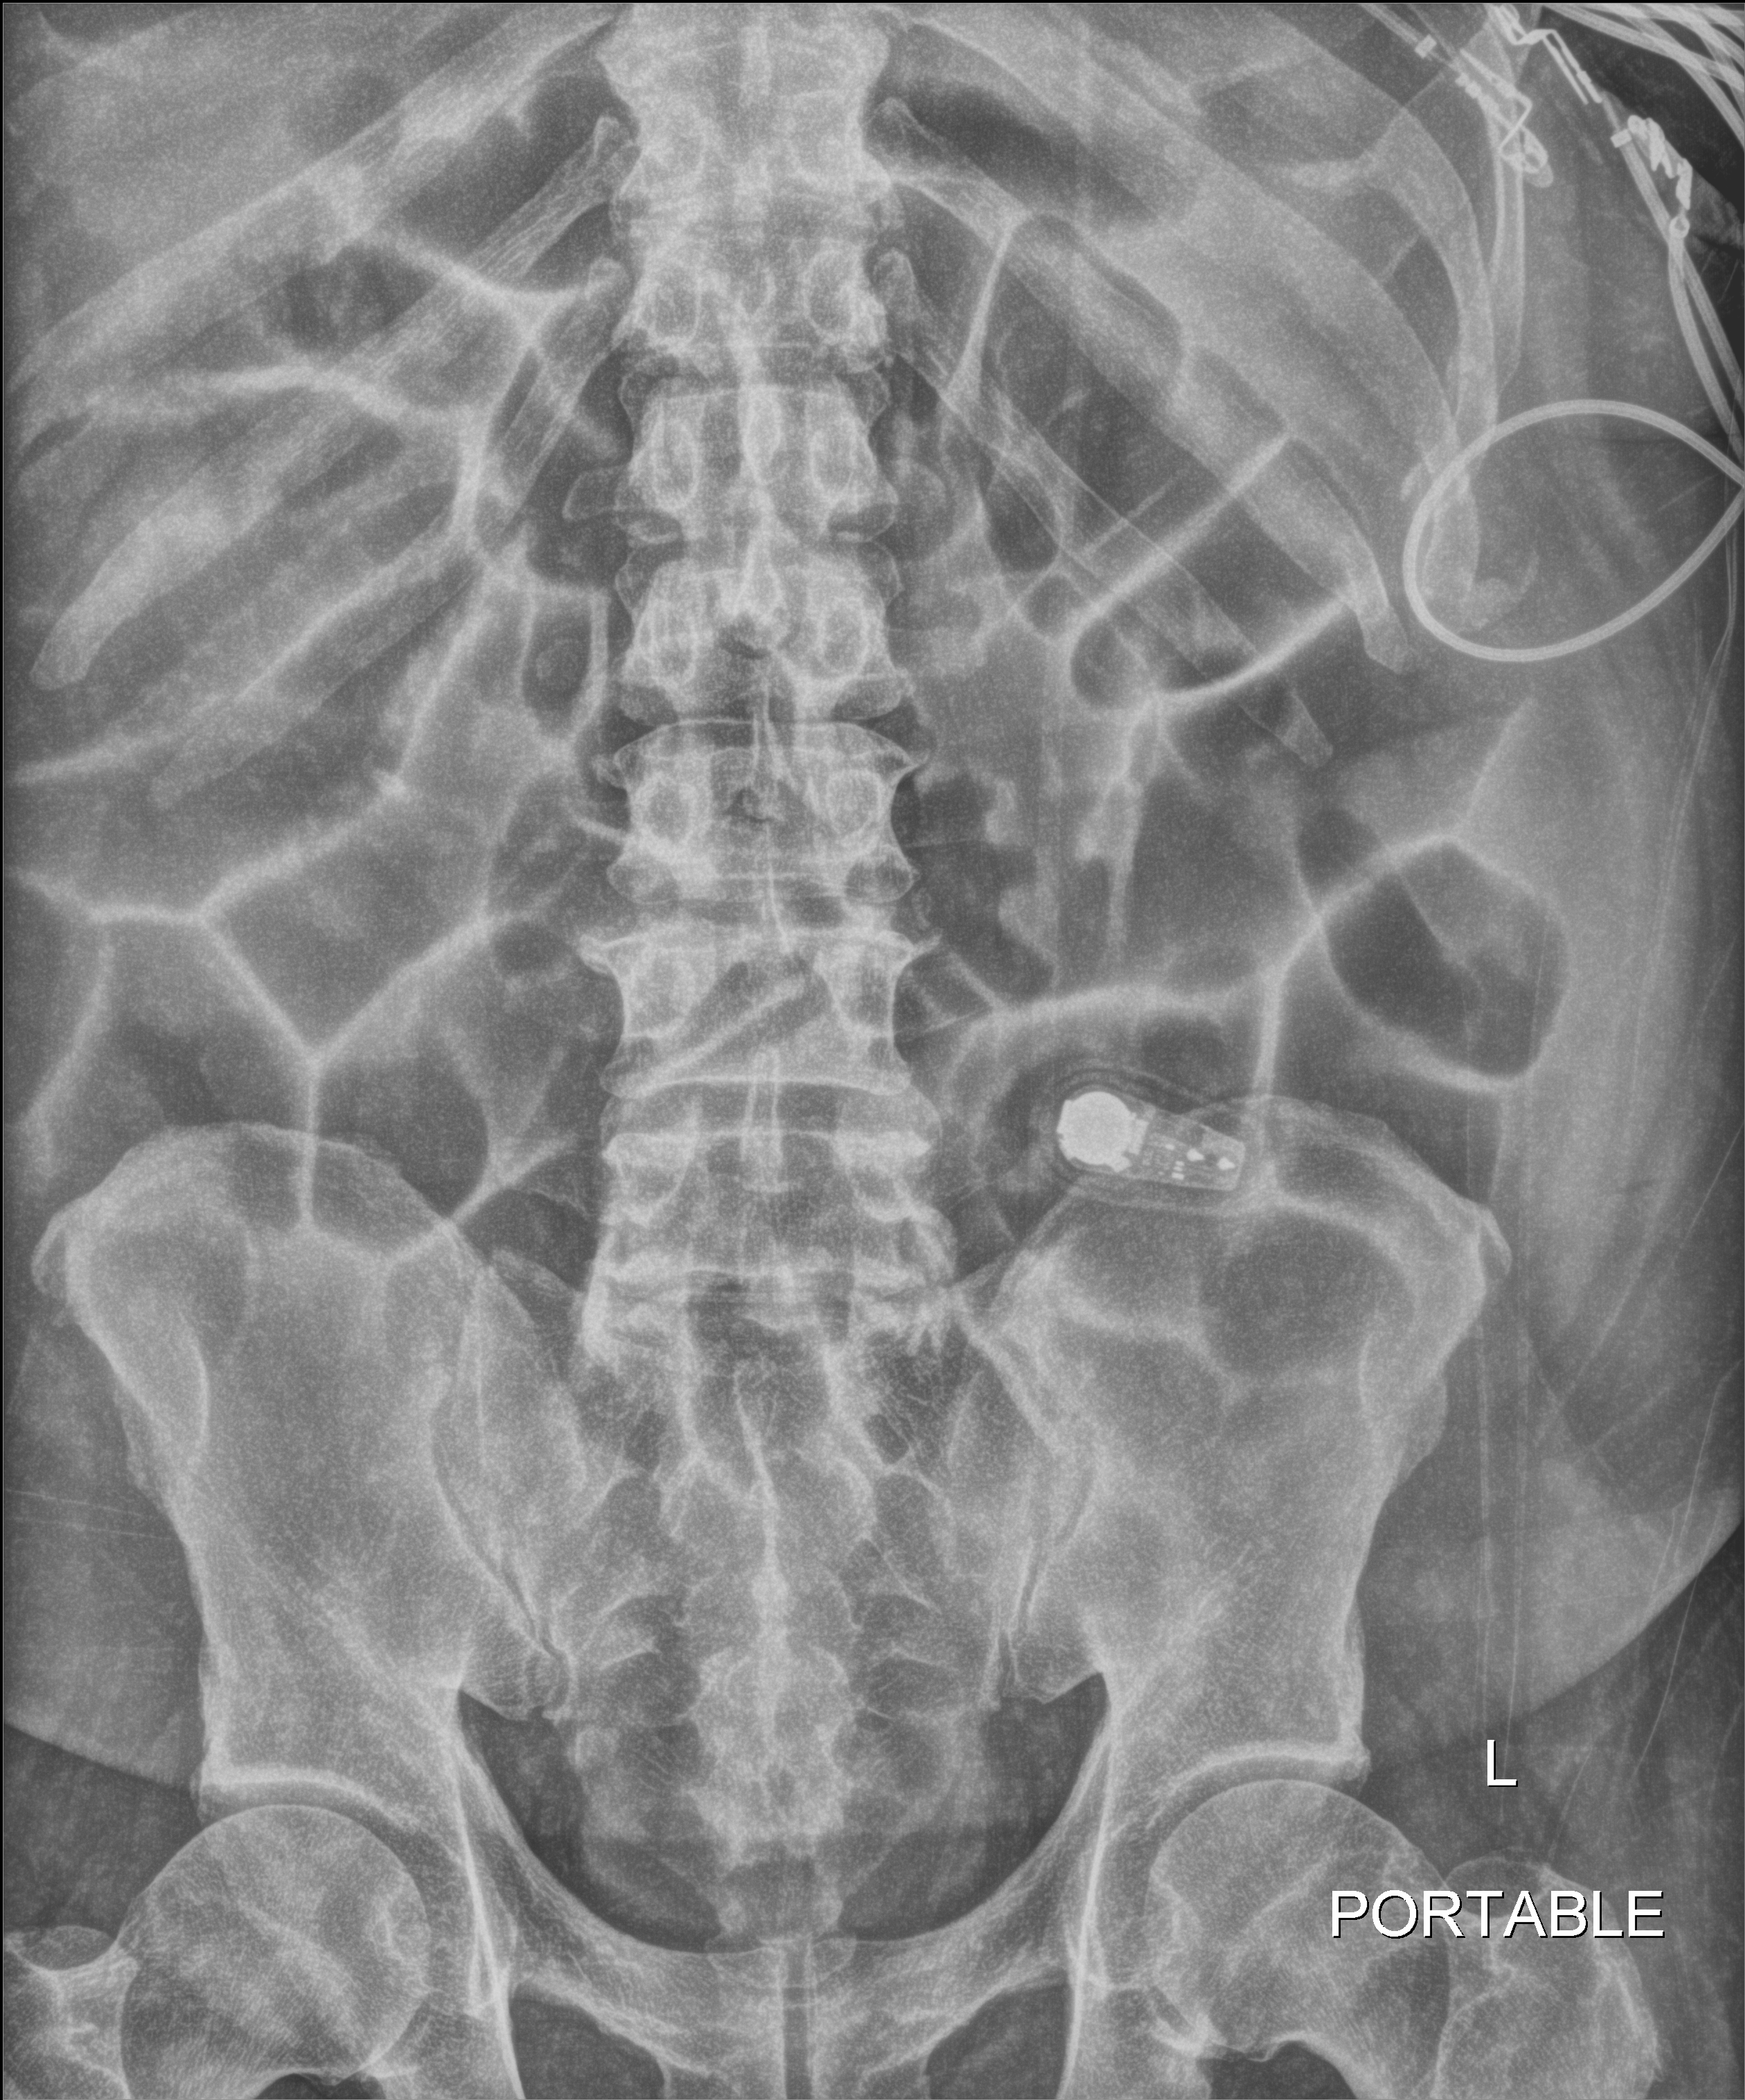
Bedside abdomen radiograph (digital radiography); anteroposterior (AP) projection. Patient hospitalised with COVID-19; male, aged 18–59 years.
From the hospital-stay record, not from the radiograph (when in the stay this image was taken is not recorded):
- mechanically ventilated during this hospital stay: yes
- admitted to intensive care during this hospital stay: yes